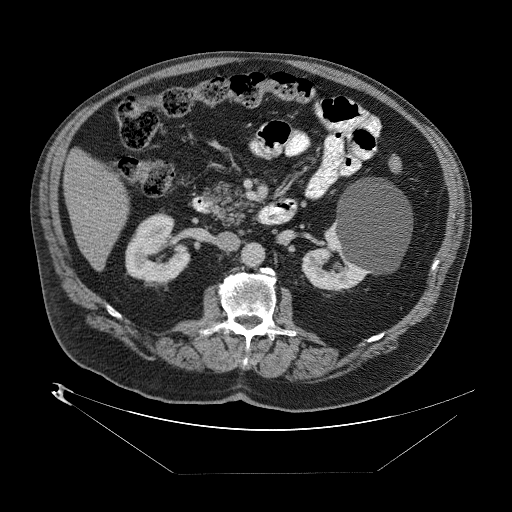
Contrast-enhanced abdominal CT (liver protocol), one axial slice. Slice 18 of 89 in the series (ordered by position). One of 2 acquisitions stored at this slice position. Soft-tissue window (W 400 / L 40 HU). 2.5 mm slice thickness. 512 × 512 image matrix, field of view 480 × 480 mm. Case-level facts recorded for this patient, not image findings: diagnosis: hepatocellular carcinoma (patient treated with transarterial chemoembolisation; whether this scan precedes or follows treatment is not stated here); TNM stage (as recorded): Stage-II; Child-Pugh class: B; tumour differentiation: moderately differentiated; tumour nodularity: multinodular.
Annotated regions visible in this slice (semi-automatic segmentation, software-assisted and operator-edited):
- abdominal aorta: box from (x=244, y=244) to (x=265, y=266) px
- liver parenchyma outside the tumour (the mass and vessels are separate outlines, so this box may not span the whole liver): (x=62, y=144)–(x=130, y=264)
- liver vessels: (x=80, y=158)–(x=97, y=233)